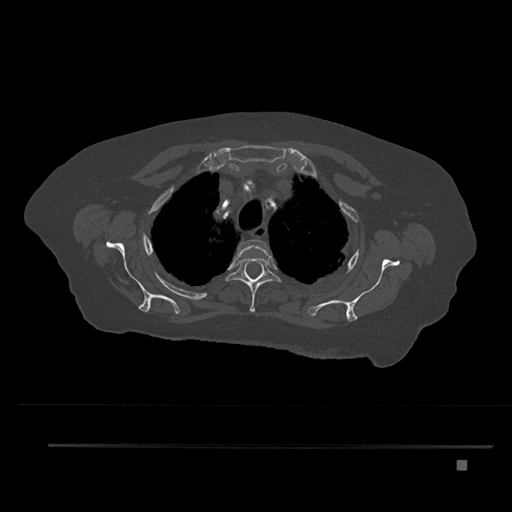
CT including the spine, one axial slice; slice 642 of 797 in the series (ordered by position); reconstruction kernel Br40s/3; 120 kVp; bone window (W 1800 / L 400 HU); 0.5 mm slice thickness; 512 × 512 image matrix, field of view 437 × 437 mm. Female patient, age 76 years. From the clinical record (not read from this slice): primary cancer: lung; vertebrae with lytic lesions (as recorded): T11, L3.
Annotated regions visible in this slice (semi-automatic segmentation, software-assisted and operator-edited):
- T2 vertebra: bounding box [x1, y1, x2, y2] px = [237, 239, 270, 258]
- T3 vertebra: [225, 257, 281, 312]